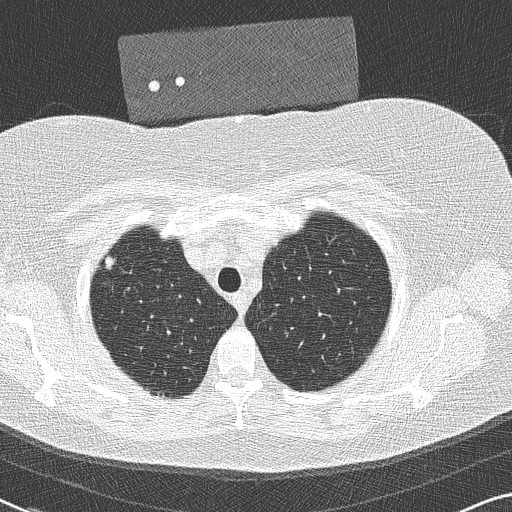
Low-dose screening chest CT, axial slice, baseline screening round, lung window (W 1500 / L -600 HU), 2 mm slice thickness, lung (sharp) reconstruction kernel (B50f), 120 kVp. Female participant, aged 58 years at enrolment. Former smoker at enrolment.
• Expert-annotated lung lesion, bounding box <92,247,131,293> (left, top, right, bottom; pixels).
• Screening reader's record for this exam: no non-calcified nodule ≥4 mm recorded.
• Official screen result: negative screen, minor abnormalities not suspicious for lung cancer.
• Later outcome: lung cancer diagnosed 846 days after this screen (after the third annual screen) — bronchiolo-alveolar adenocarcinoma, NOS, right upper lobe, well differentiated (G1), stage IA (AJCC 6th edition), 9 mm at pathology.